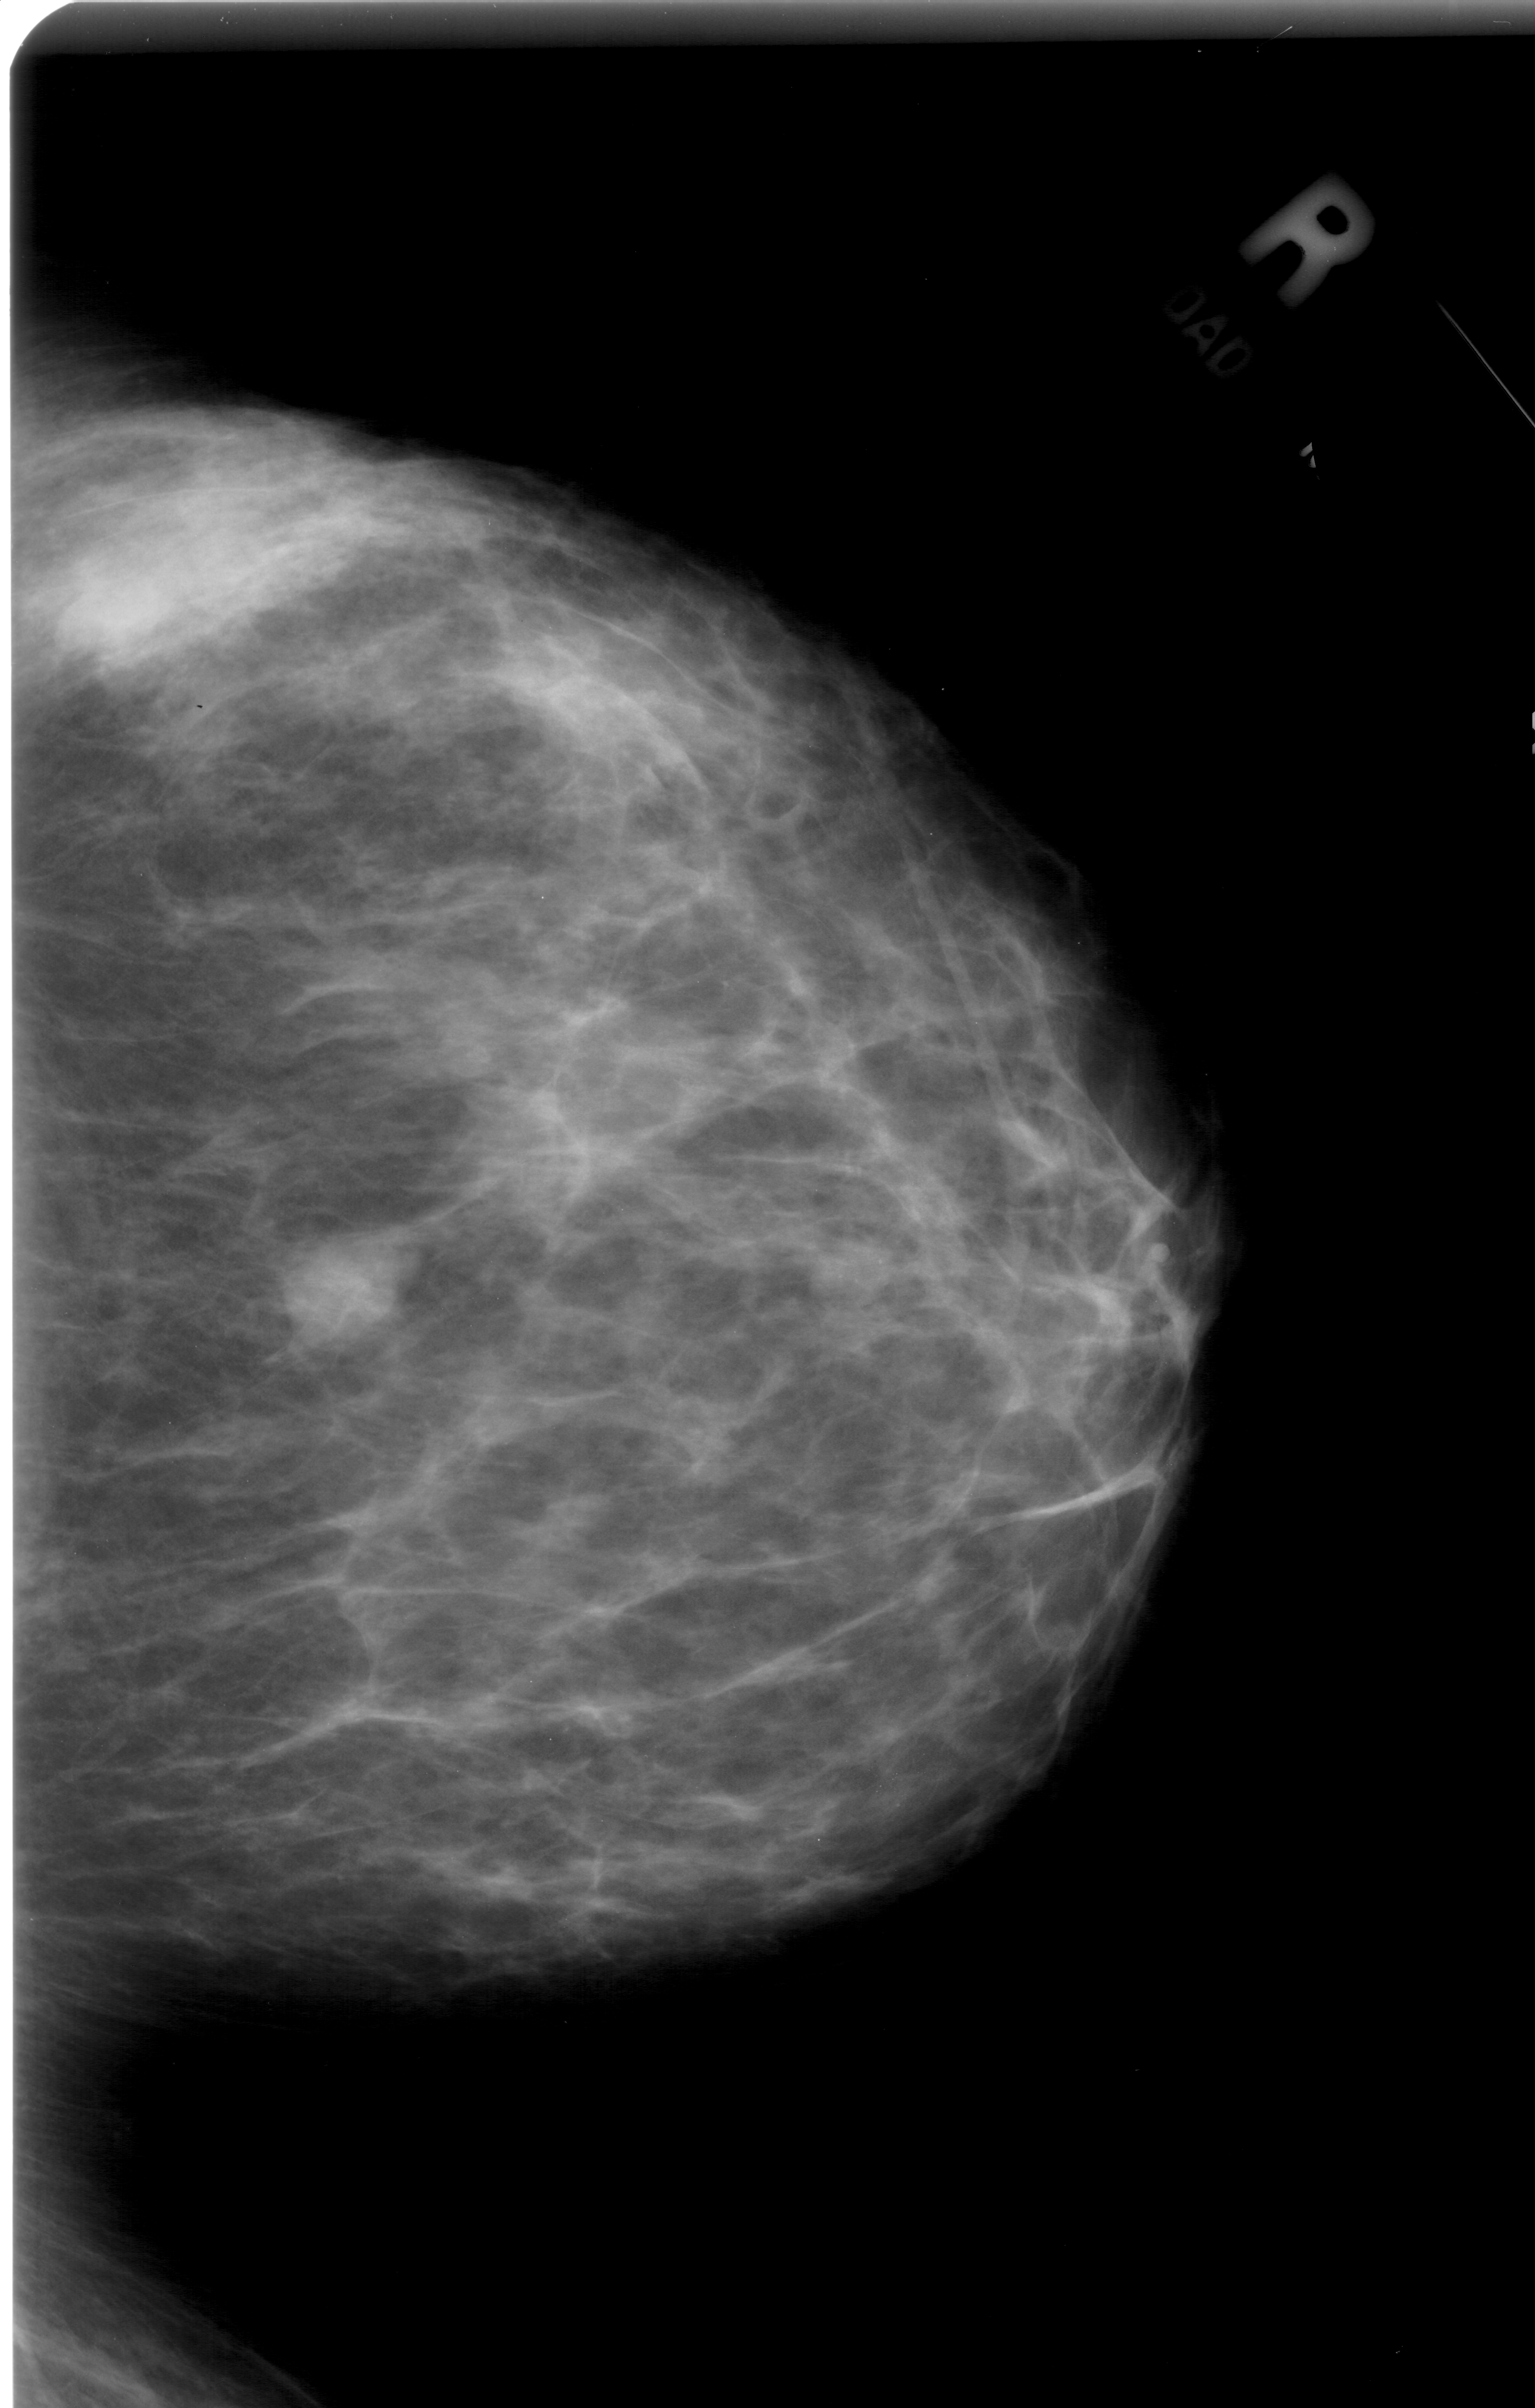
Scanned film-screen mammogram. Right breast. Craniocaudal (CC) view. BI-RADS breast density category 1 (scale 1–4). 1535 × 2408 image matrix.
Expert-marked regions of interest on this image (one box per marked abnormality):
- mass, shape lobulated, margins ill defined; BI-RADS assessment category 4; subtlety rating 3 on a 1 (subtle) to 5 (obvious) scale; pathology result (as recorded, not read from the image): benign: bounding box [x1, y1, x2, y2] px = [298, 1239, 406, 1340]